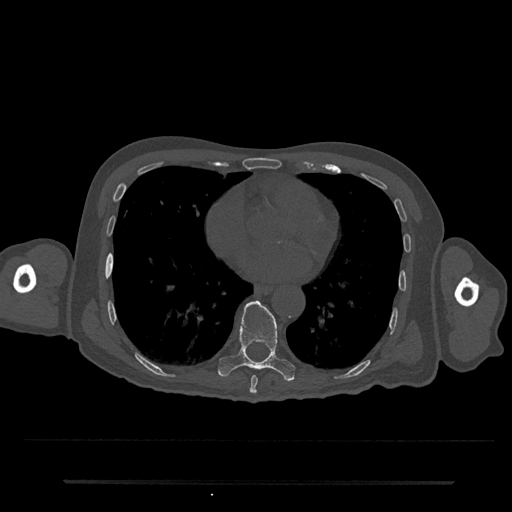
CT including the spine, one axial slice; slice 375 of 797 in the series (ordered by position); reconstruction kernel Br40s/3; 120 kVp; bone window (W 1800 / L 400 HU); 0.5 mm slice thickness; 512 × 512 image matrix, field of view 427 × 427 mm. Patient: male, 74 years. From the clinical record (not read from this slice): primary cancer: prostate.
Structures marked on this image (semi-automatic segmentation, software-assisted and operator-edited):
- T8 vertebra: box from (x=249, y=376) to (x=258, y=394) px
- T9 vertebra: (x=218, y=301)–(x=295, y=381)